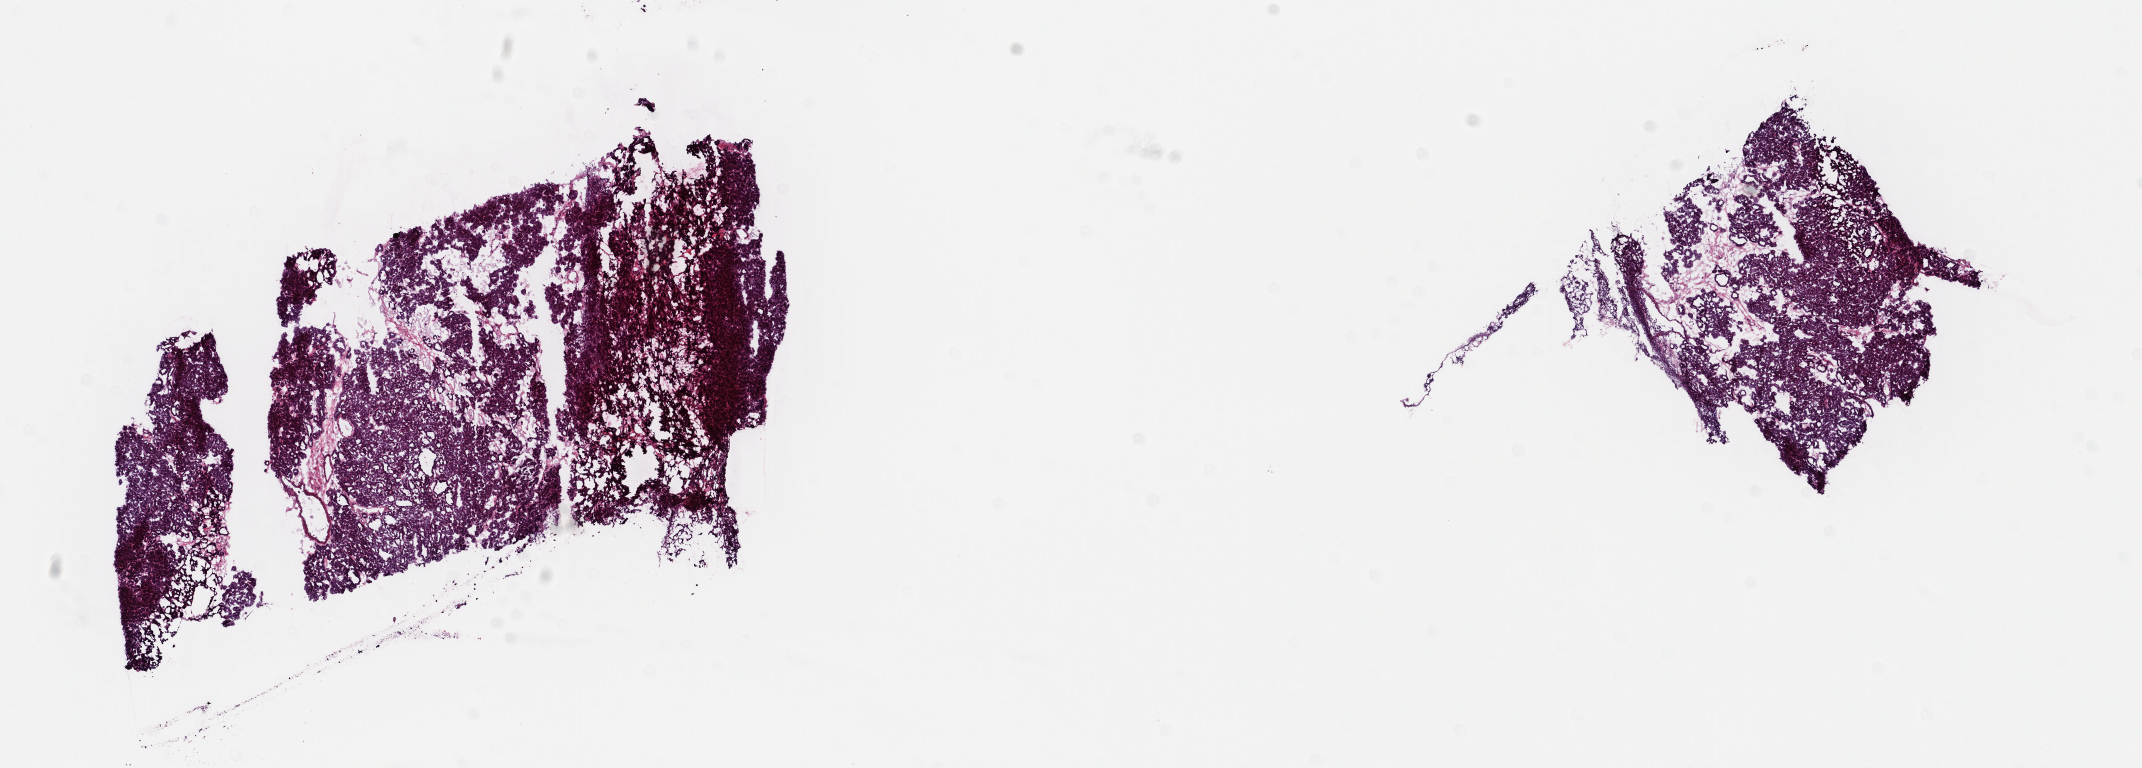
Digitized H&E-stained tissue section (whole slide), a low-resolution overview of the entire scanned area, about 16.8 x 6.0 mm (acquisition: 40x scan). Frozen section from the top of the tissue portion. Primary tumour sample from the thyroid. Female, age 73 years at initial diagnosis. Pathologist review of this section (percent, as recorded): tumour cells 85%, tumour nuclei 95%, normal cells 10%, stromal cells 5%, necrosis 0%. Inflammatory infiltration, as recorded: lymphocyte infiltration 0%, monocyte infiltration 1%, neutrophil infiltration 0%.
Pathologic diagnosis: Papillary carcinoma, follicular variant (thyroid gland). Laterality: left. AJCC pathologic stage: II.